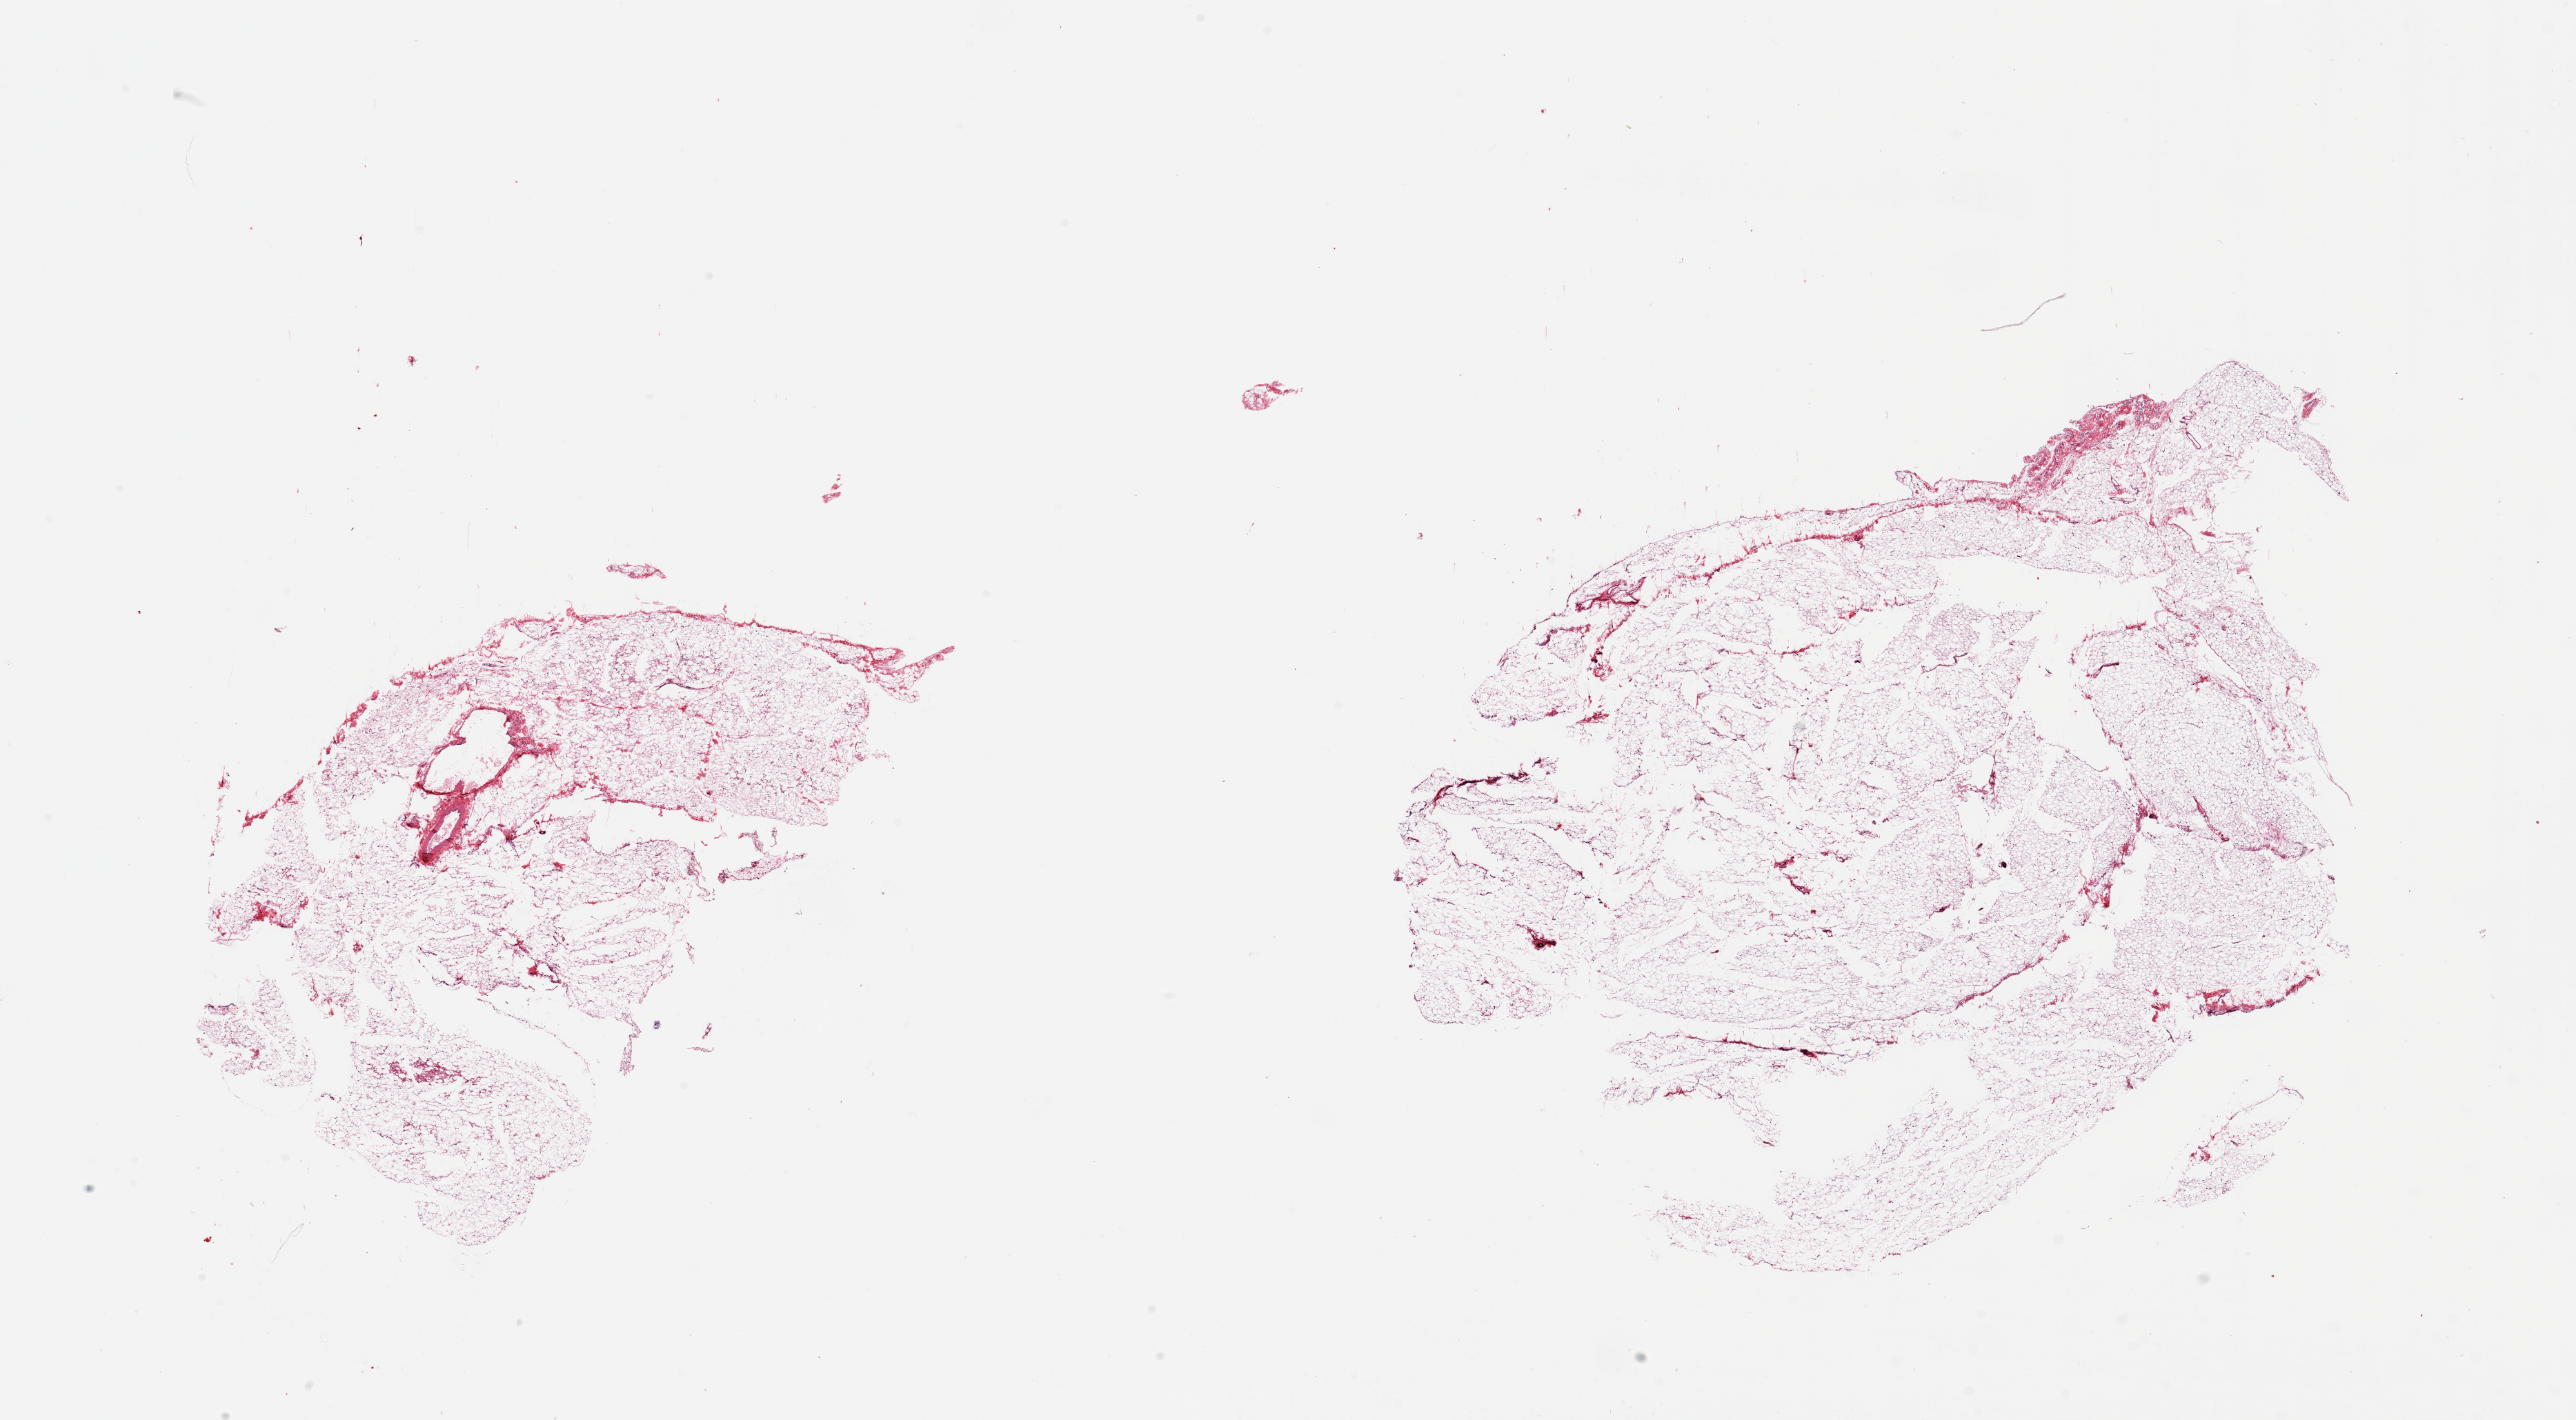
Hematoxylin and eosin (H&E) whole-slide image, shown as a low-resolution overview of the whole scanned area (about 29.5 x 16.3 mm). PAXgene-fixed, paraffin-embedded tissue. Sampled site (target tissue): omentum. Tissue donor sample. Female donor.
Reviewer comment on this tissue sample: 2 pieces; focal preserved mesothelial lining.